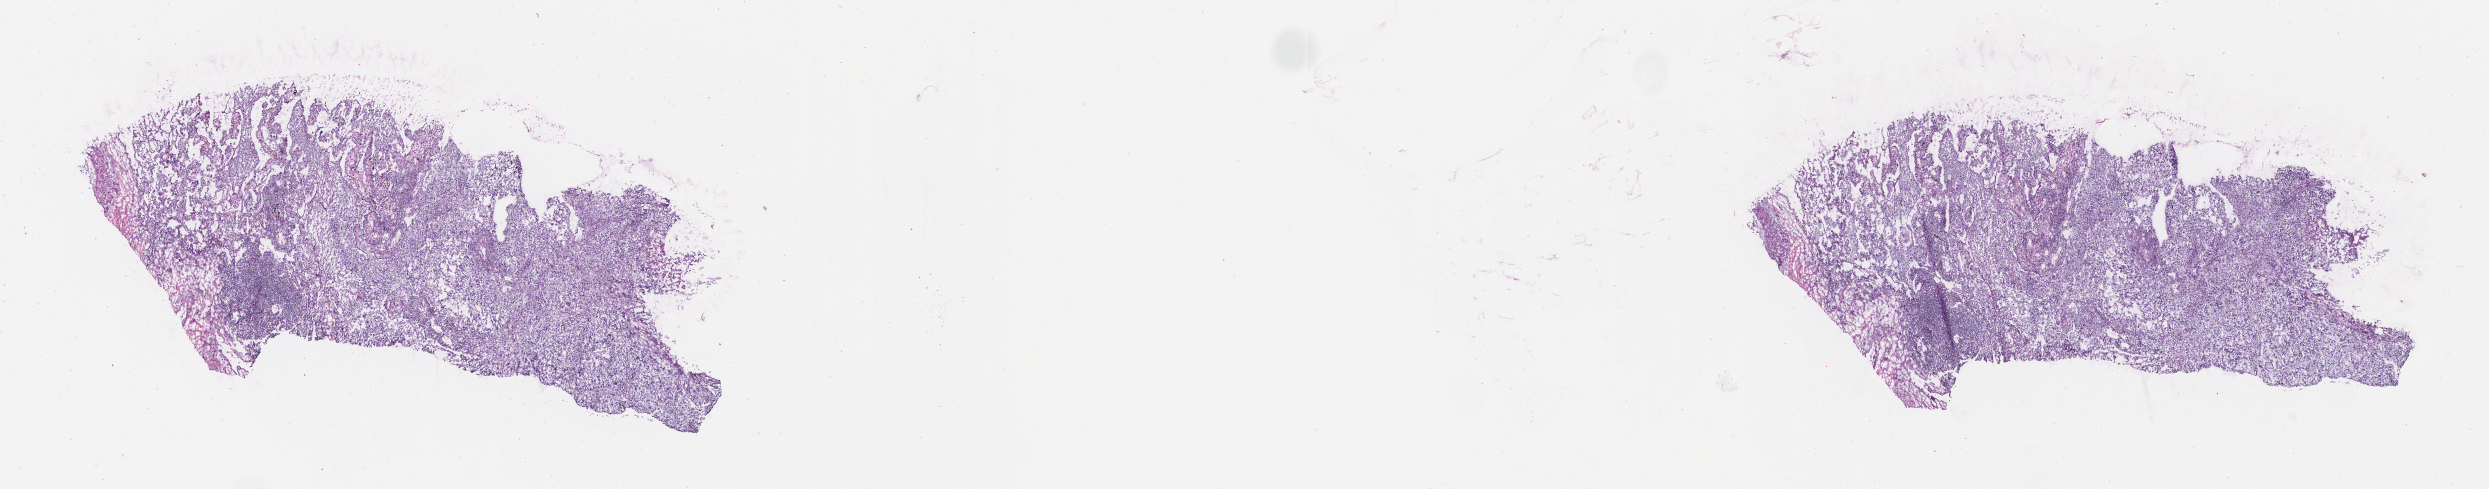
Whole-slide image, haematoxylin and eosin stain — low-resolution overview of the scanned area, about 20.1 x 4.0 mm, frozen section, specimen: primary tumor, site: upper lobe of left lung. Patient: female, age 59 years. Slide review estimates, as recorded: tumor cells 59%, tumor nuclei 70%, stromal cells 18%, necrosis 11%, normal cells 12%. Inflammatory infiltration, as recorded: lymphocyte infiltration 16%, monocyte infiltration 10%, neutrophil infiltration 1%.
AJCC pathologic stage: Stage IV. Histologic diagnosis: Adenocarcinoma, NOS. Section: top of the tissue portion.